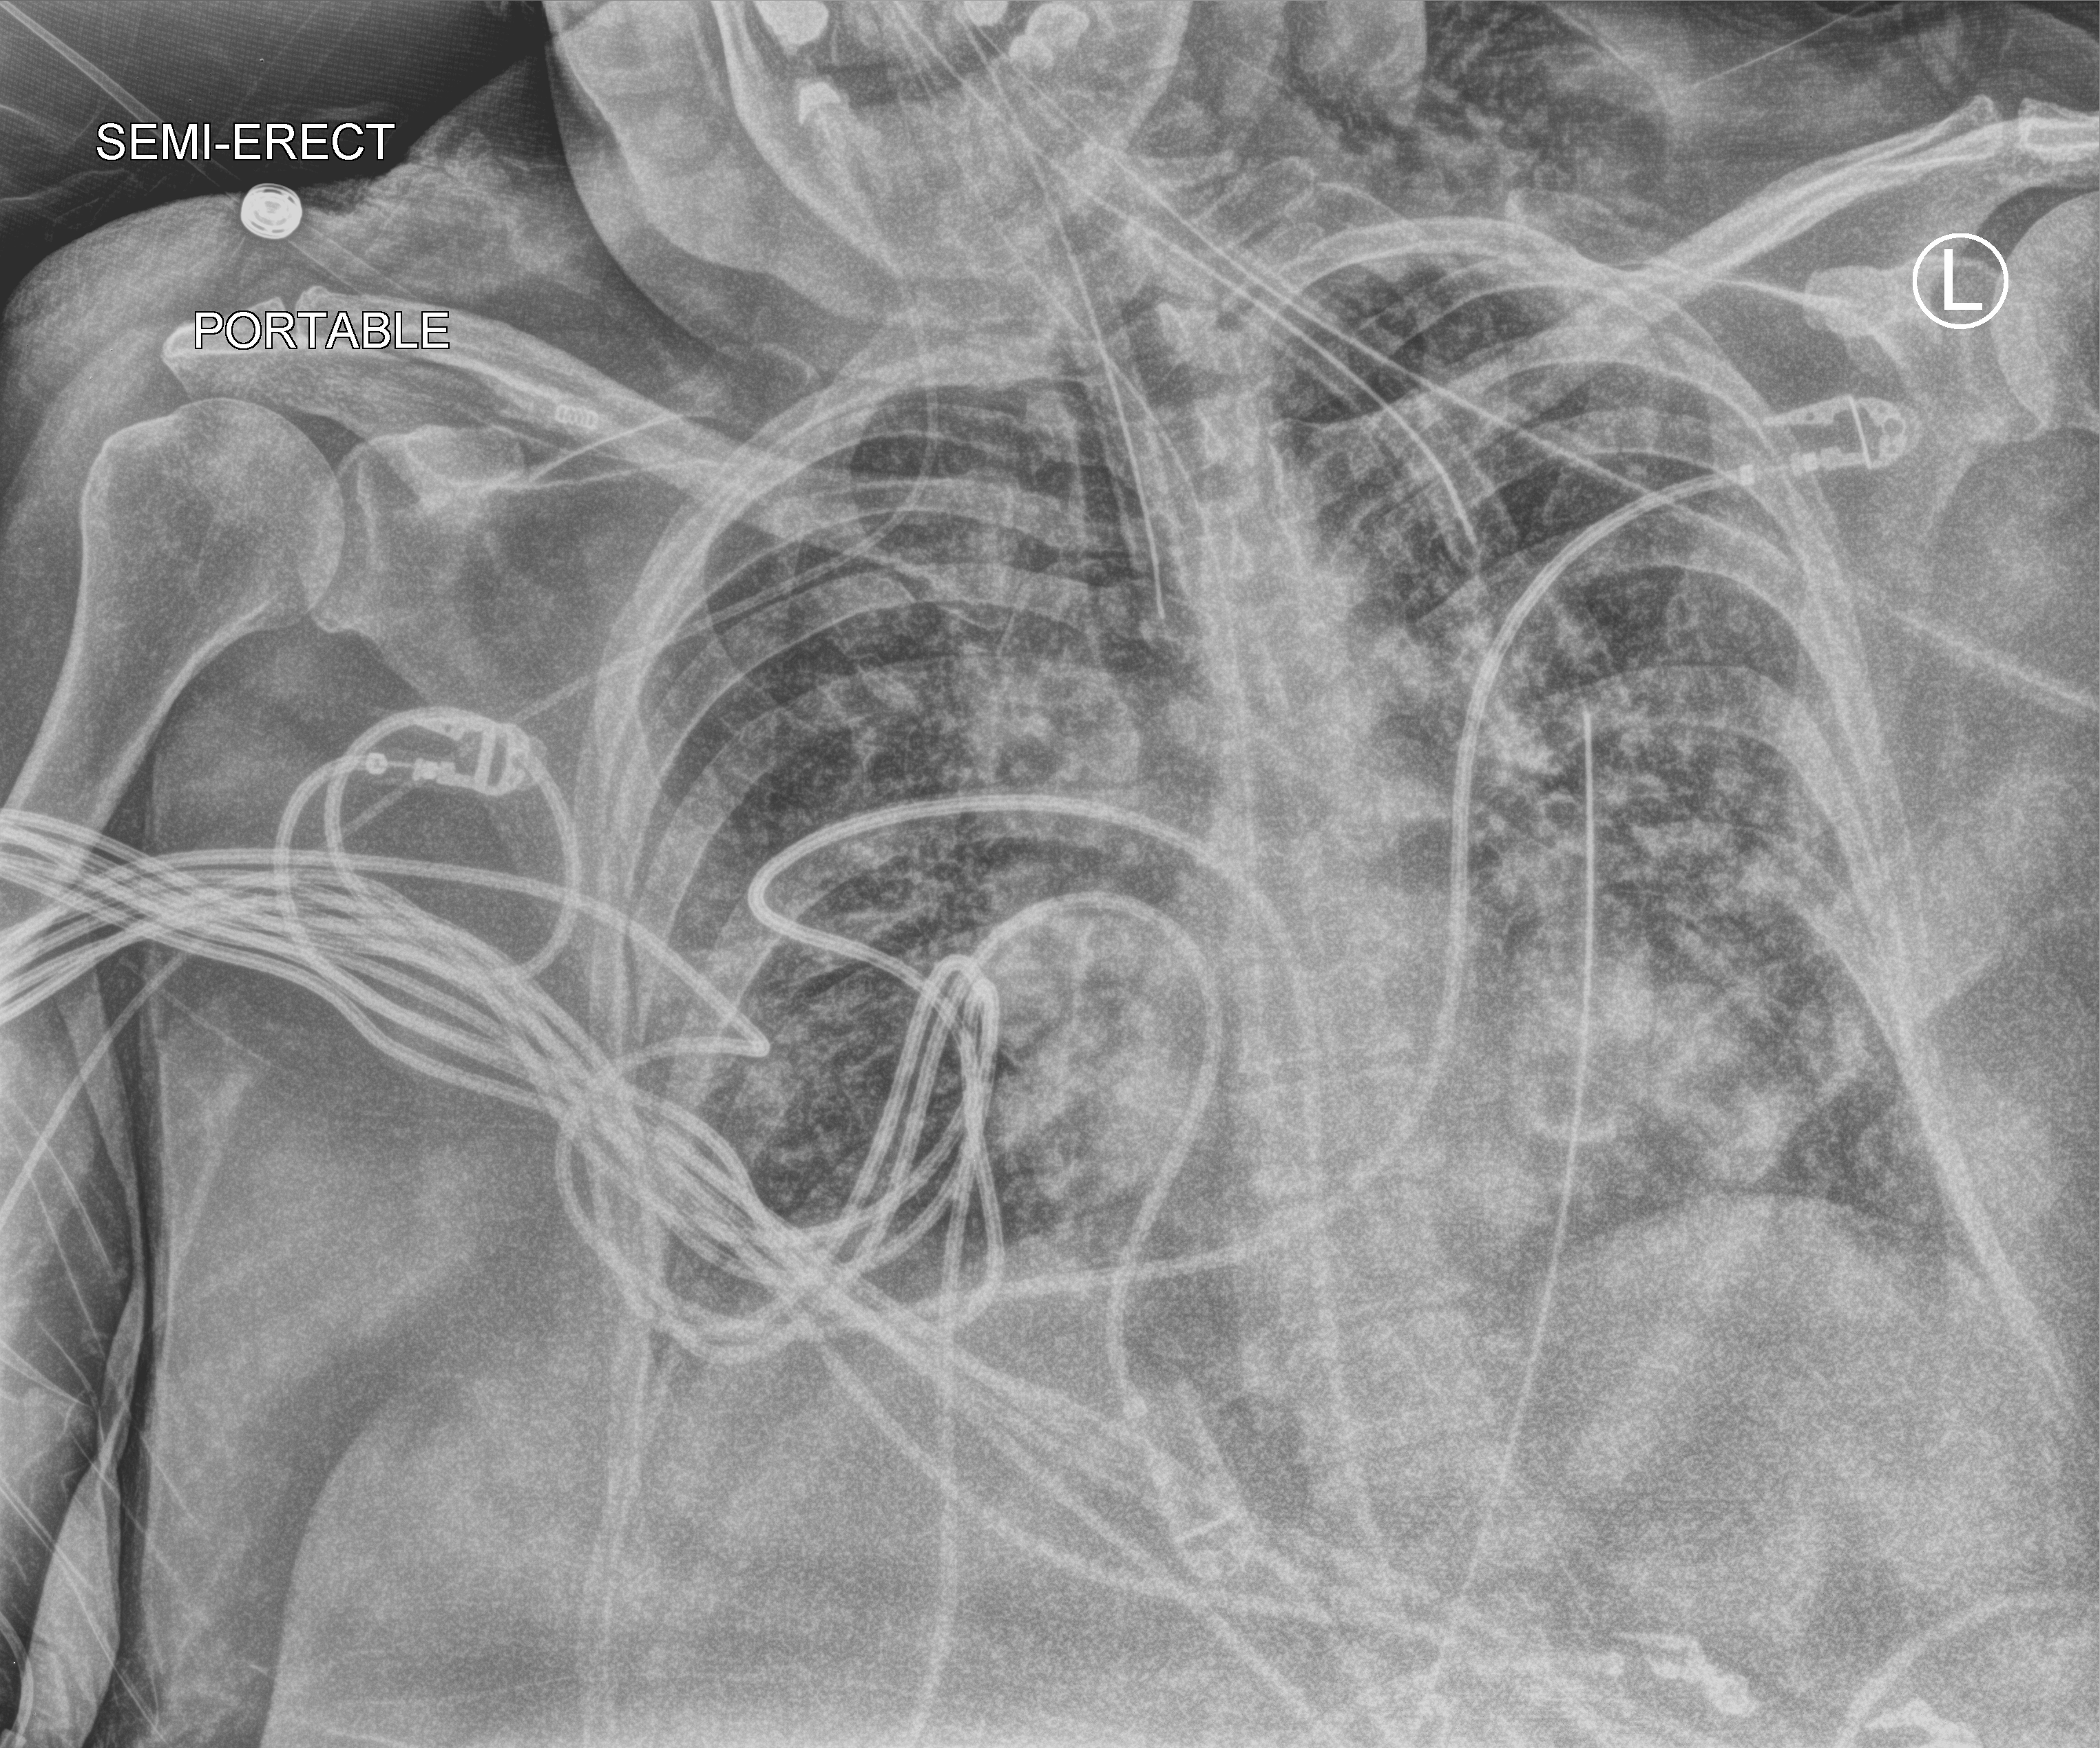
Chest X-ray (portable). Patient hospitalised with COVID-19; female, aged 60–74 years.
Hospital-stay facts (about this admission, not read from this image; timing relative to this image not recorded):
- mechanically ventilated during this hospital stay: yes
- length of hospital stay: 45 days
- admitted to intensive care during this hospital stay: yes